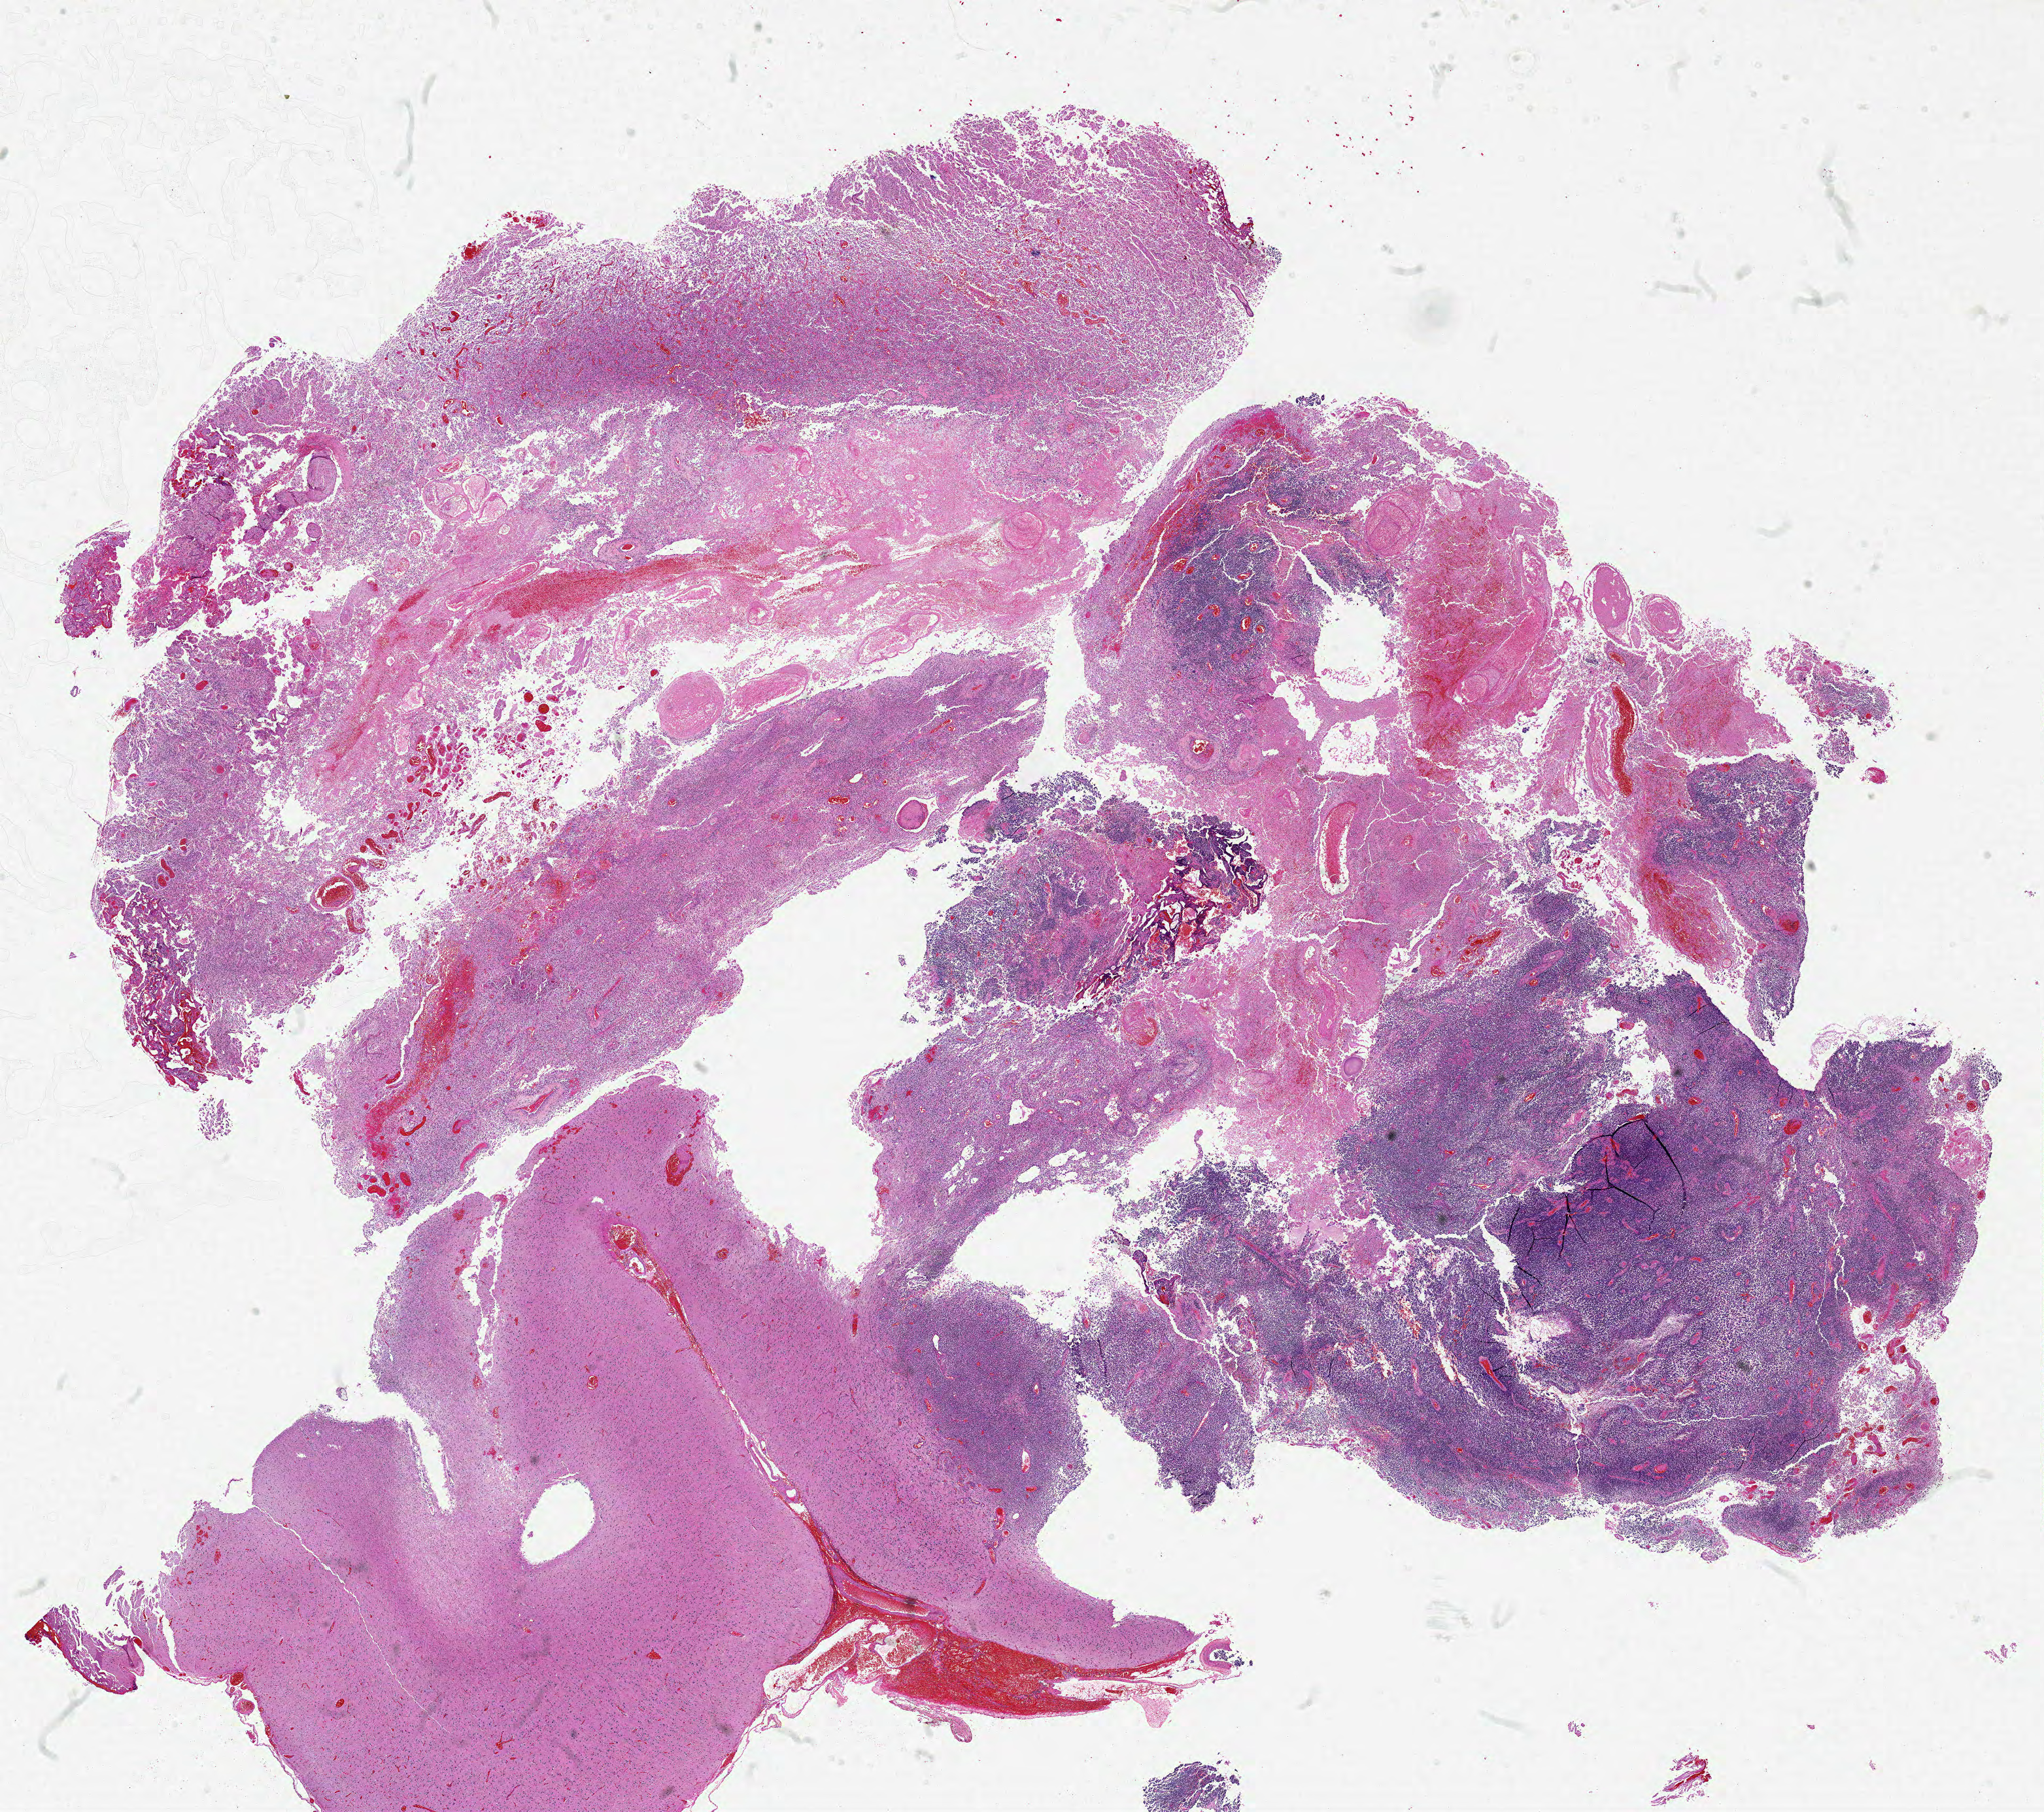
Whole-slide histology image, H&E-stained, a low-resolution overview of the entire scanned area, about 25.0 x 22.1 mm (from a 20x scan), formalin-fixed paraffin-embedded (FFPE) diagnostic section, primary tumour sample from the brain. Patient: male, age at initial diagnosis 46 years.
• diagnosis: Glioblastoma